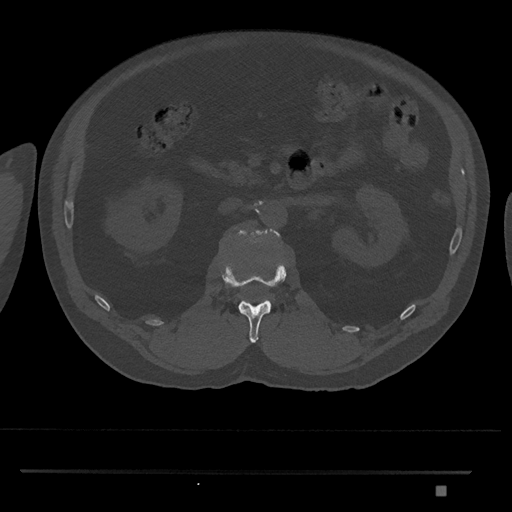
CT including the spine, one axial slice. Position 799 of 1134 along the scan axis. 120 kVp. Bone window (W 1800 / L 400 HU). 0.5 mm slice thickness. 512 × 512 image matrix. Patient: male, 65 years. Case-level facts recorded for this patient, not image findings: primary cancer: prostate.
Annotated regions visible in this slice (semi-automatic segmentation, software-assisted and operator-edited):
- L1 vertebra: bounding box [x1, y1, x2, y2] px = [221, 264, 287, 343]
- L2 vertebra: [228, 228, 280, 298]